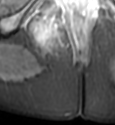
MRI of an extremity soft-tissue mass, one axial slice; position 33 of 49 along the scan axis; STIR; MR volume resampled by the dataset authors to the PET/CT grid (not the native acquisition matrix); 115 × 125 image matrix, field of view 112 × 122 mm. Female patient. Case-level facts recorded for this patient, not image findings: histological type: epithelioid sarcoma; grade: intermediate; site of the primary tumour: right buttock.
Structures marked on this image (expert contour drawn on MRI and transferred to this co-registered scan by the dataset authors):
- gross tumour volume including surrounding oedema: bounding box <35,16,59,42> (left, top, right, bottom; pixels)